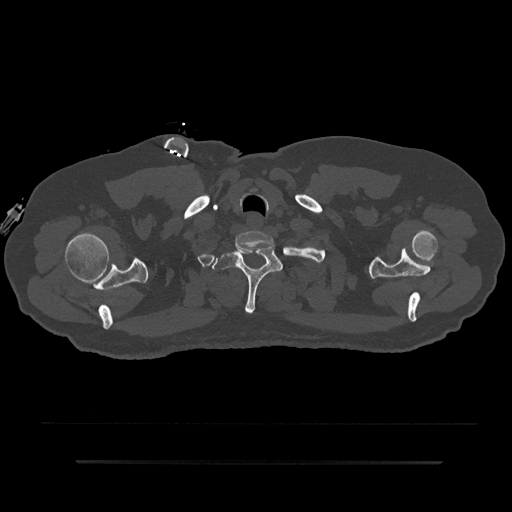
CT including the spine, one axial slice. 120 kVp. Bone window (W 1800 / L 400 HU). 0.5 mm slice thickness. 512 × 512 image matrix, field of view 464 × 464 mm. Patient: male, 59 years. From the clinical record (not read from this slice): primary cancer: bile ducts; vertebrae with lytic lesions (as recorded): T10.
Outlined on this slice (semi-automatic segmentation, software-assisted and operator-edited):
- T1 vertebra: bounding box [x1, y1, x2, y2] px = [212, 246, 283, 314]